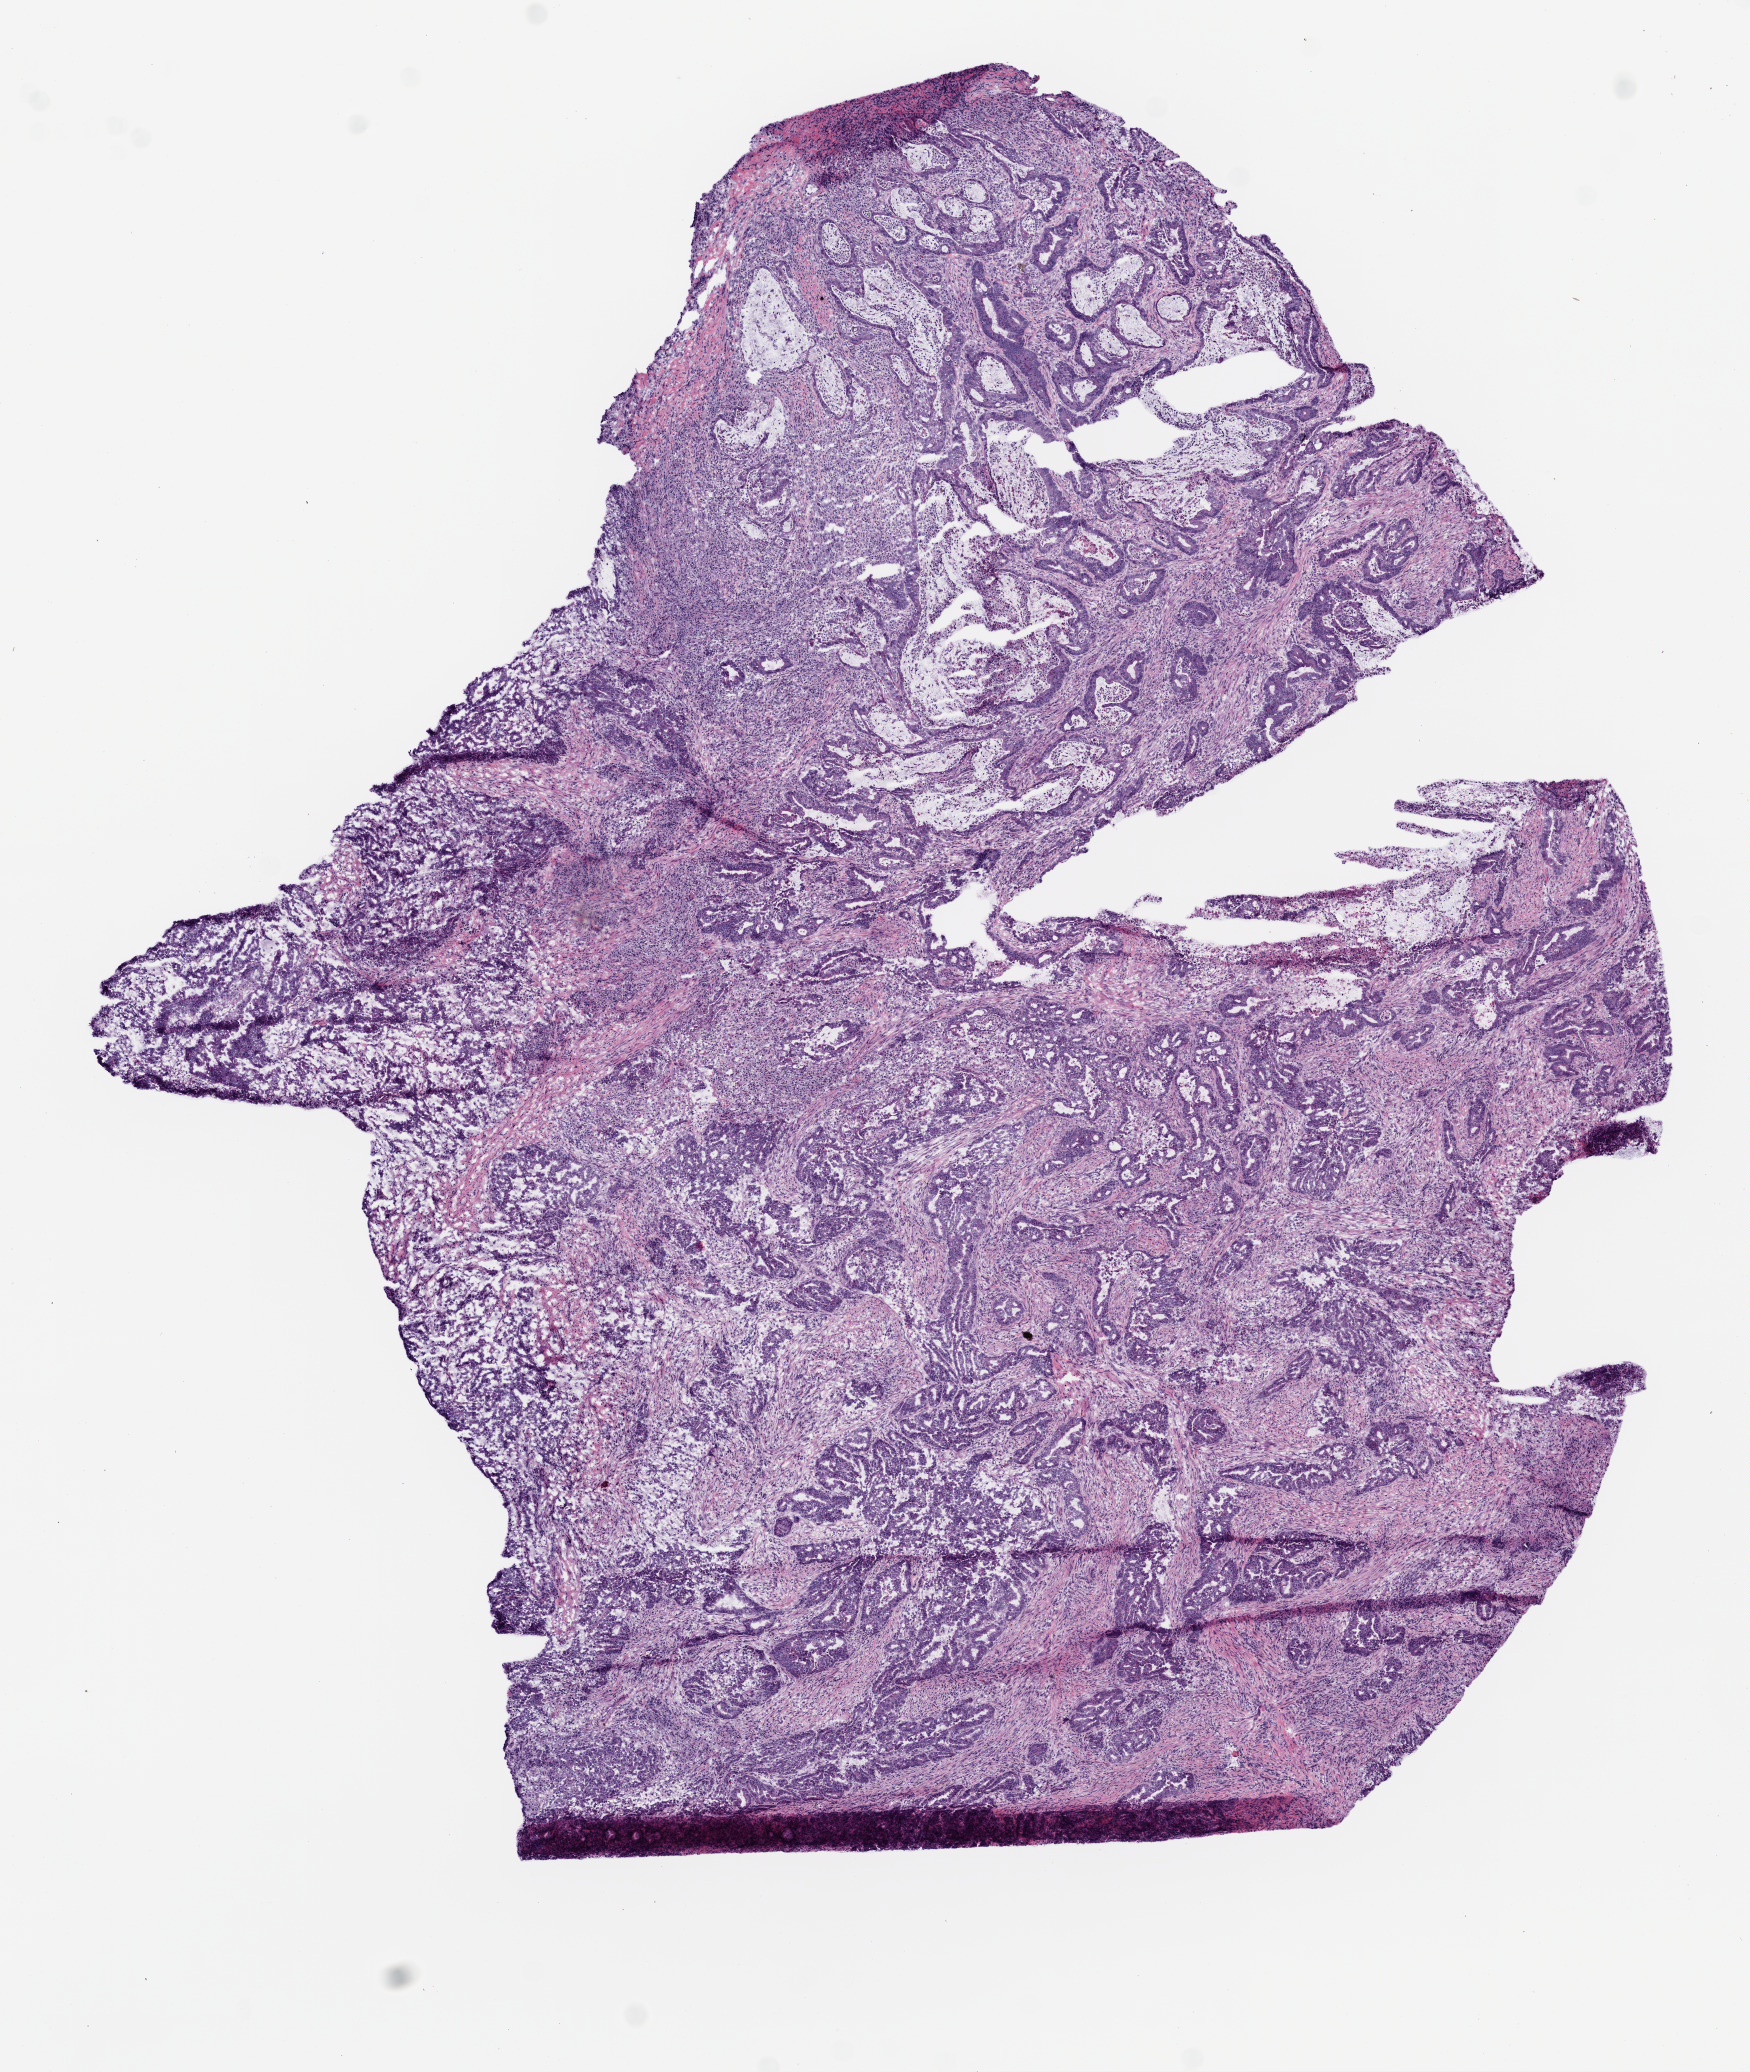
Whole-slide histology image, Hematoxylin and eosin (H&E) stained — whole scanned area (about 7.0 x 8.3 mm, acquisition: 20x scan) shown as a low-resolution overview. Frozen section. Primary tumour sample from the stomach. Male, age 83 years at initial diagnosis. Histologic grade: G2 (moderately differentiated). Composition of this section per pathologist review: tumour cells 70%, tumour nuclei 65%, normal cells 0%, stromal cells 25%, necrosis 8%. Inflammatory infiltration, as recorded: lymphocyte infiltration 15%, neutrophil infiltration 10%.
* TNM: T2 N2 M0
* AJCC pathologic stage: IIIA (5th edition)
* pathologic diagnosis: Adenocarcinoma, intestinal type